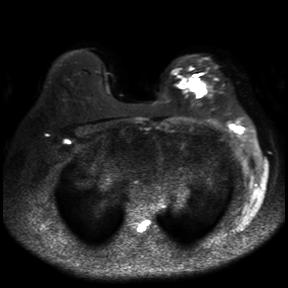
Breast MRI, one axial slice; slice 22 of 30 in the series (ordered by position); diffusion-weighted series; image 2 of 4 stored at this slice position (different b-values; order by instance number); 3 T; 4 mm slice thickness; 288 × 288 image matrix, field of view 360 × 360 mm. Female patient.
Structures marked on this image (manually delineated by an expert):
- tumour on diffusion-weighted imaging: box from (x=189, y=79) to (x=203, y=97) px